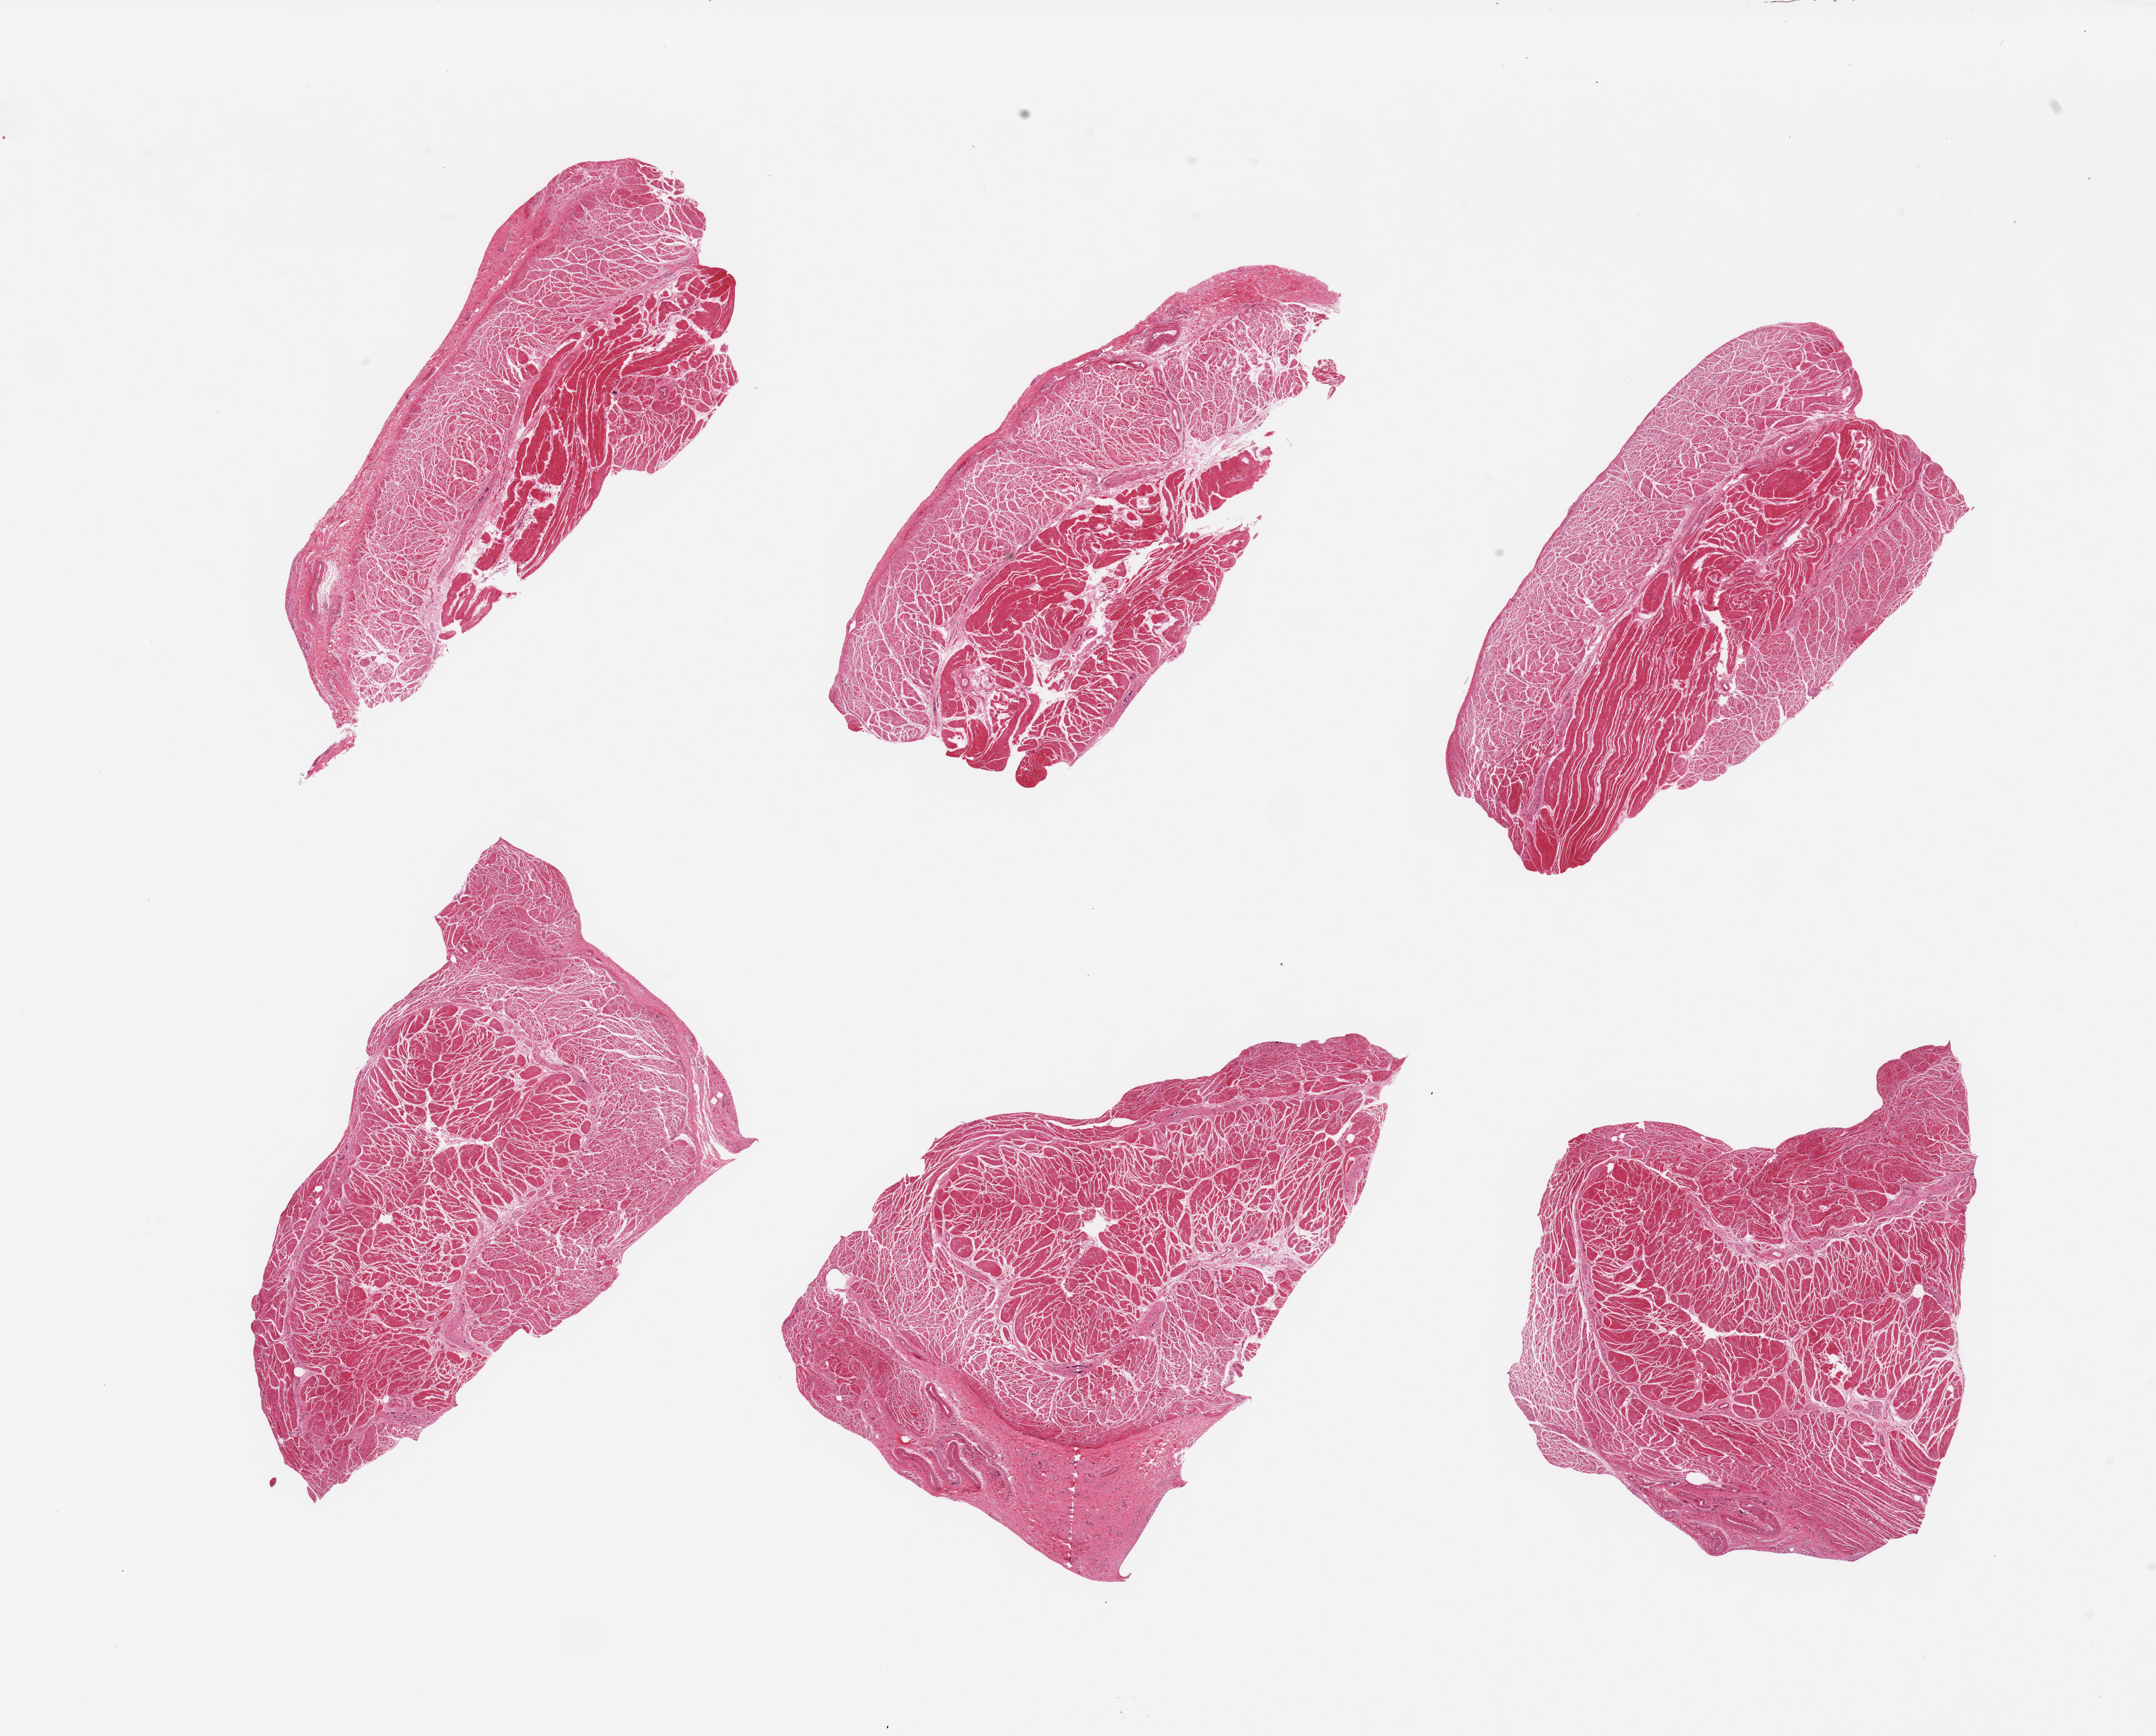
Digitized hematoxylin and eosin (H&E)-stained section, low-resolution overview of the scanned area, about 25.6 x 20.6 mm (from a 20x scan), PAXgene-fixed, paraffin-embedded tissue, sampled site (target tissue): esophageal muscle, tissue donor sample.
• review note (as recorded): 6 pieces, confirmed target muscularis